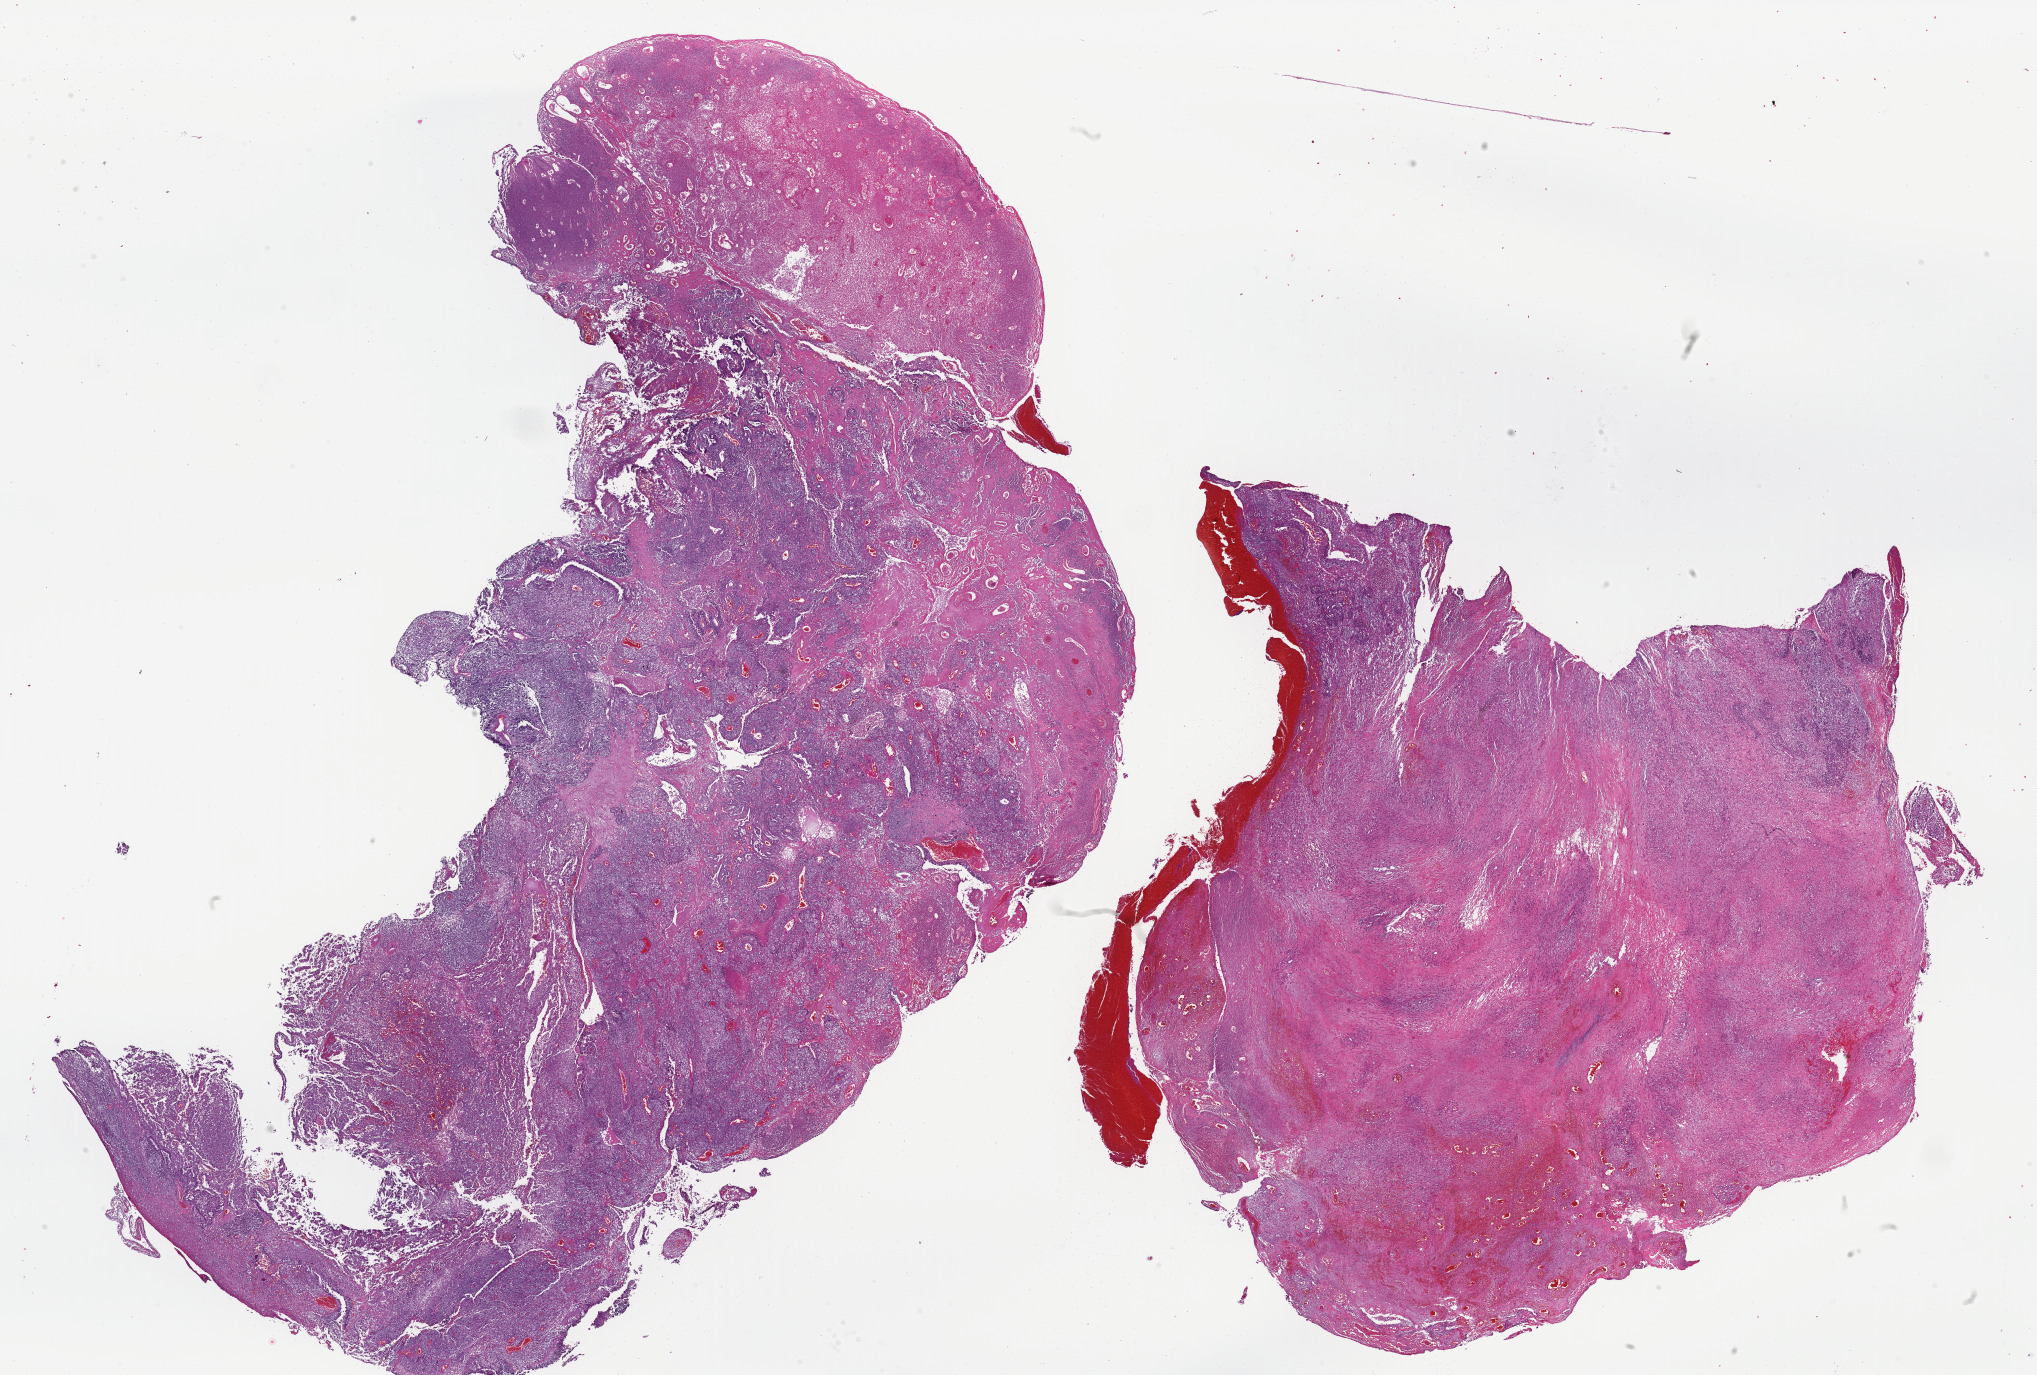
Digitized H&E-stained tissue section (whole slide), a low-resolution overview of the entire scanned area, about 32.1 x 21.7 mm. Formalin-fixed paraffin-embedded (FFPE) diagnostic section. Uterus, primary tumour sample. Female, age 75 years at initial diagnosis.
FIGO stage: IIIC1. Pathologic diagnosis: Carcinosarcoma, NOS.